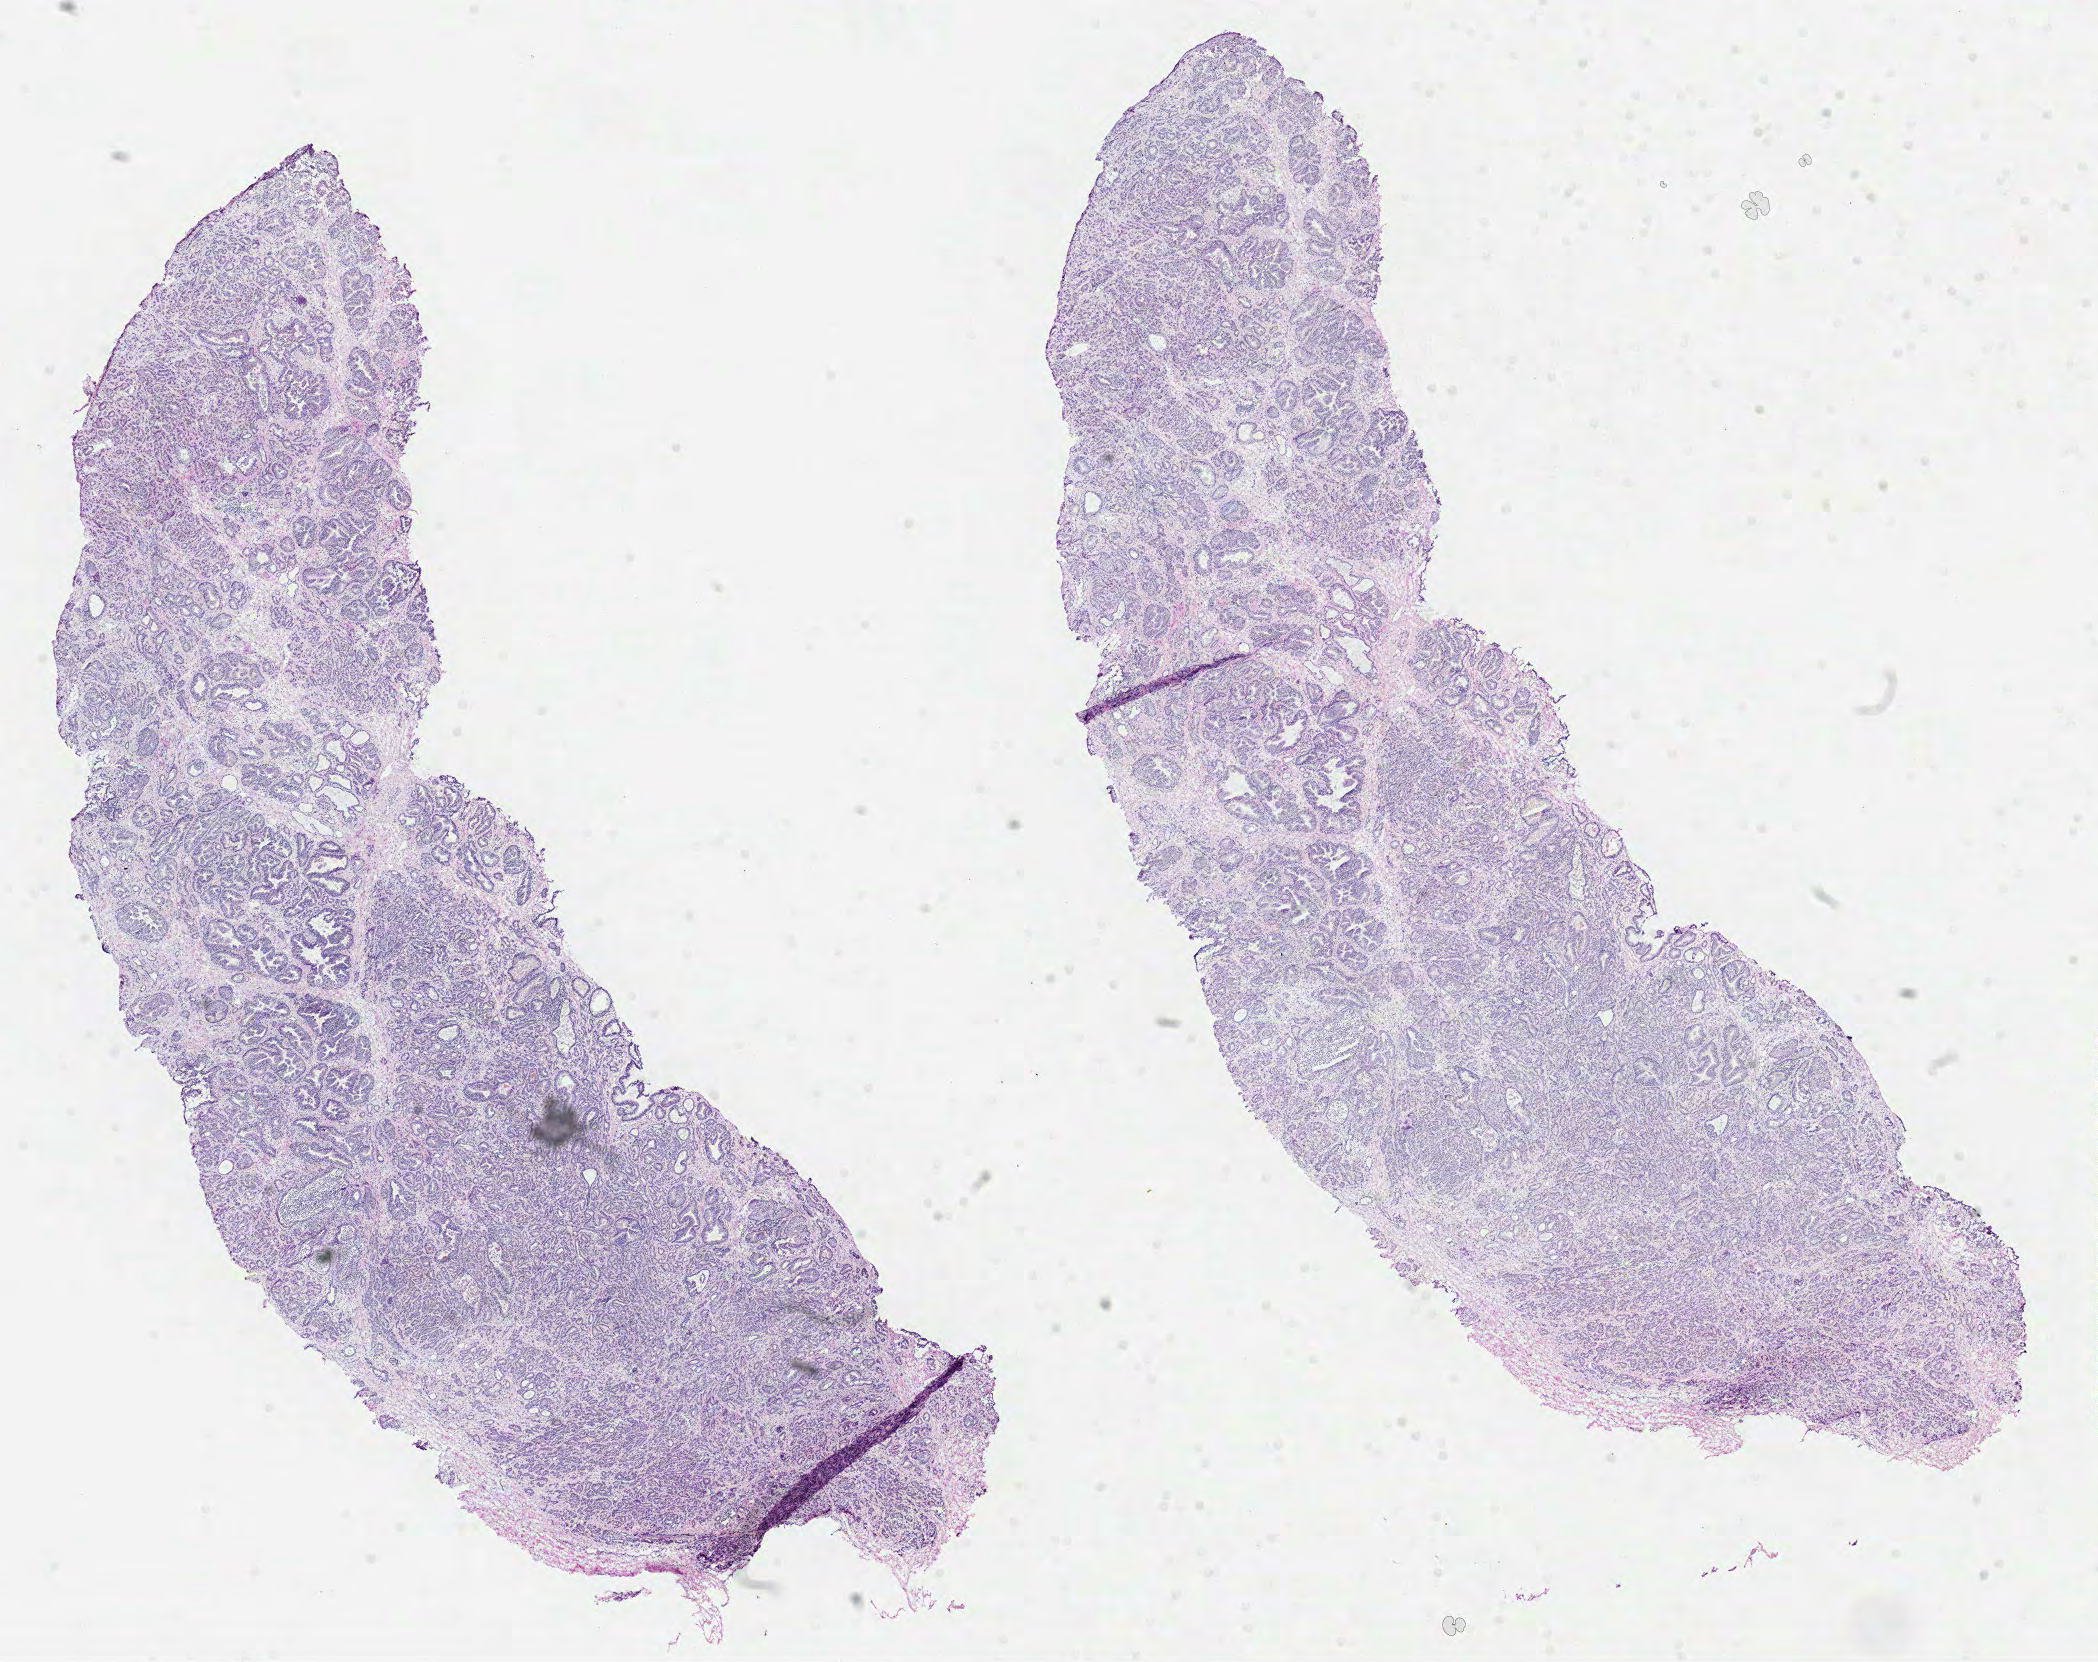
Digitized H&E-stained tissue section (whole slide), whole scanned area (about 16.9 x 13.4 mm, slide scanned at 40x) shown as a low-resolution overview, formalin-fixed paraffin-embedded (FFPE) diagnostic section, sample: primary tumour, prostate. Male patient; age at initial diagnosis 64 years. Gleason score: 7 (4+3).
Laterality: bilateral. Pathologic diagnosis: Acinar cell carcinoma (prostate gland). Lymph nodes positive (case pathology): 0 of 2 examined.